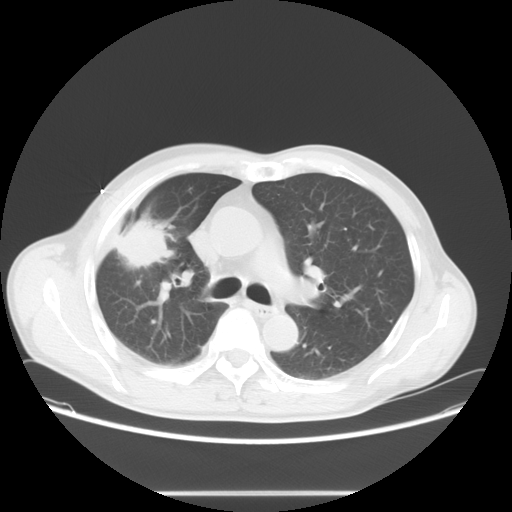
Chest CT, one axial slice. Slice 45 of 71 in the series (ordered by position). Reconstruction kernel STANDARD. 120 kVp. Lung window (W 1500 / L -600 HU). 512 × 512 image matrix, field of view 392 × 392 mm. Patient: male, 67 years. Case-level facts recorded for this patient, not image findings: clinical TNM (as recorded): T2 N0 M0.
Structures marked on this image (rectangle marked by the reading radiologist):
- lung tumour (recorded histology: adenocarcinoma): bounding box <113,219,172,268> (left, top, right, bottom; pixels)